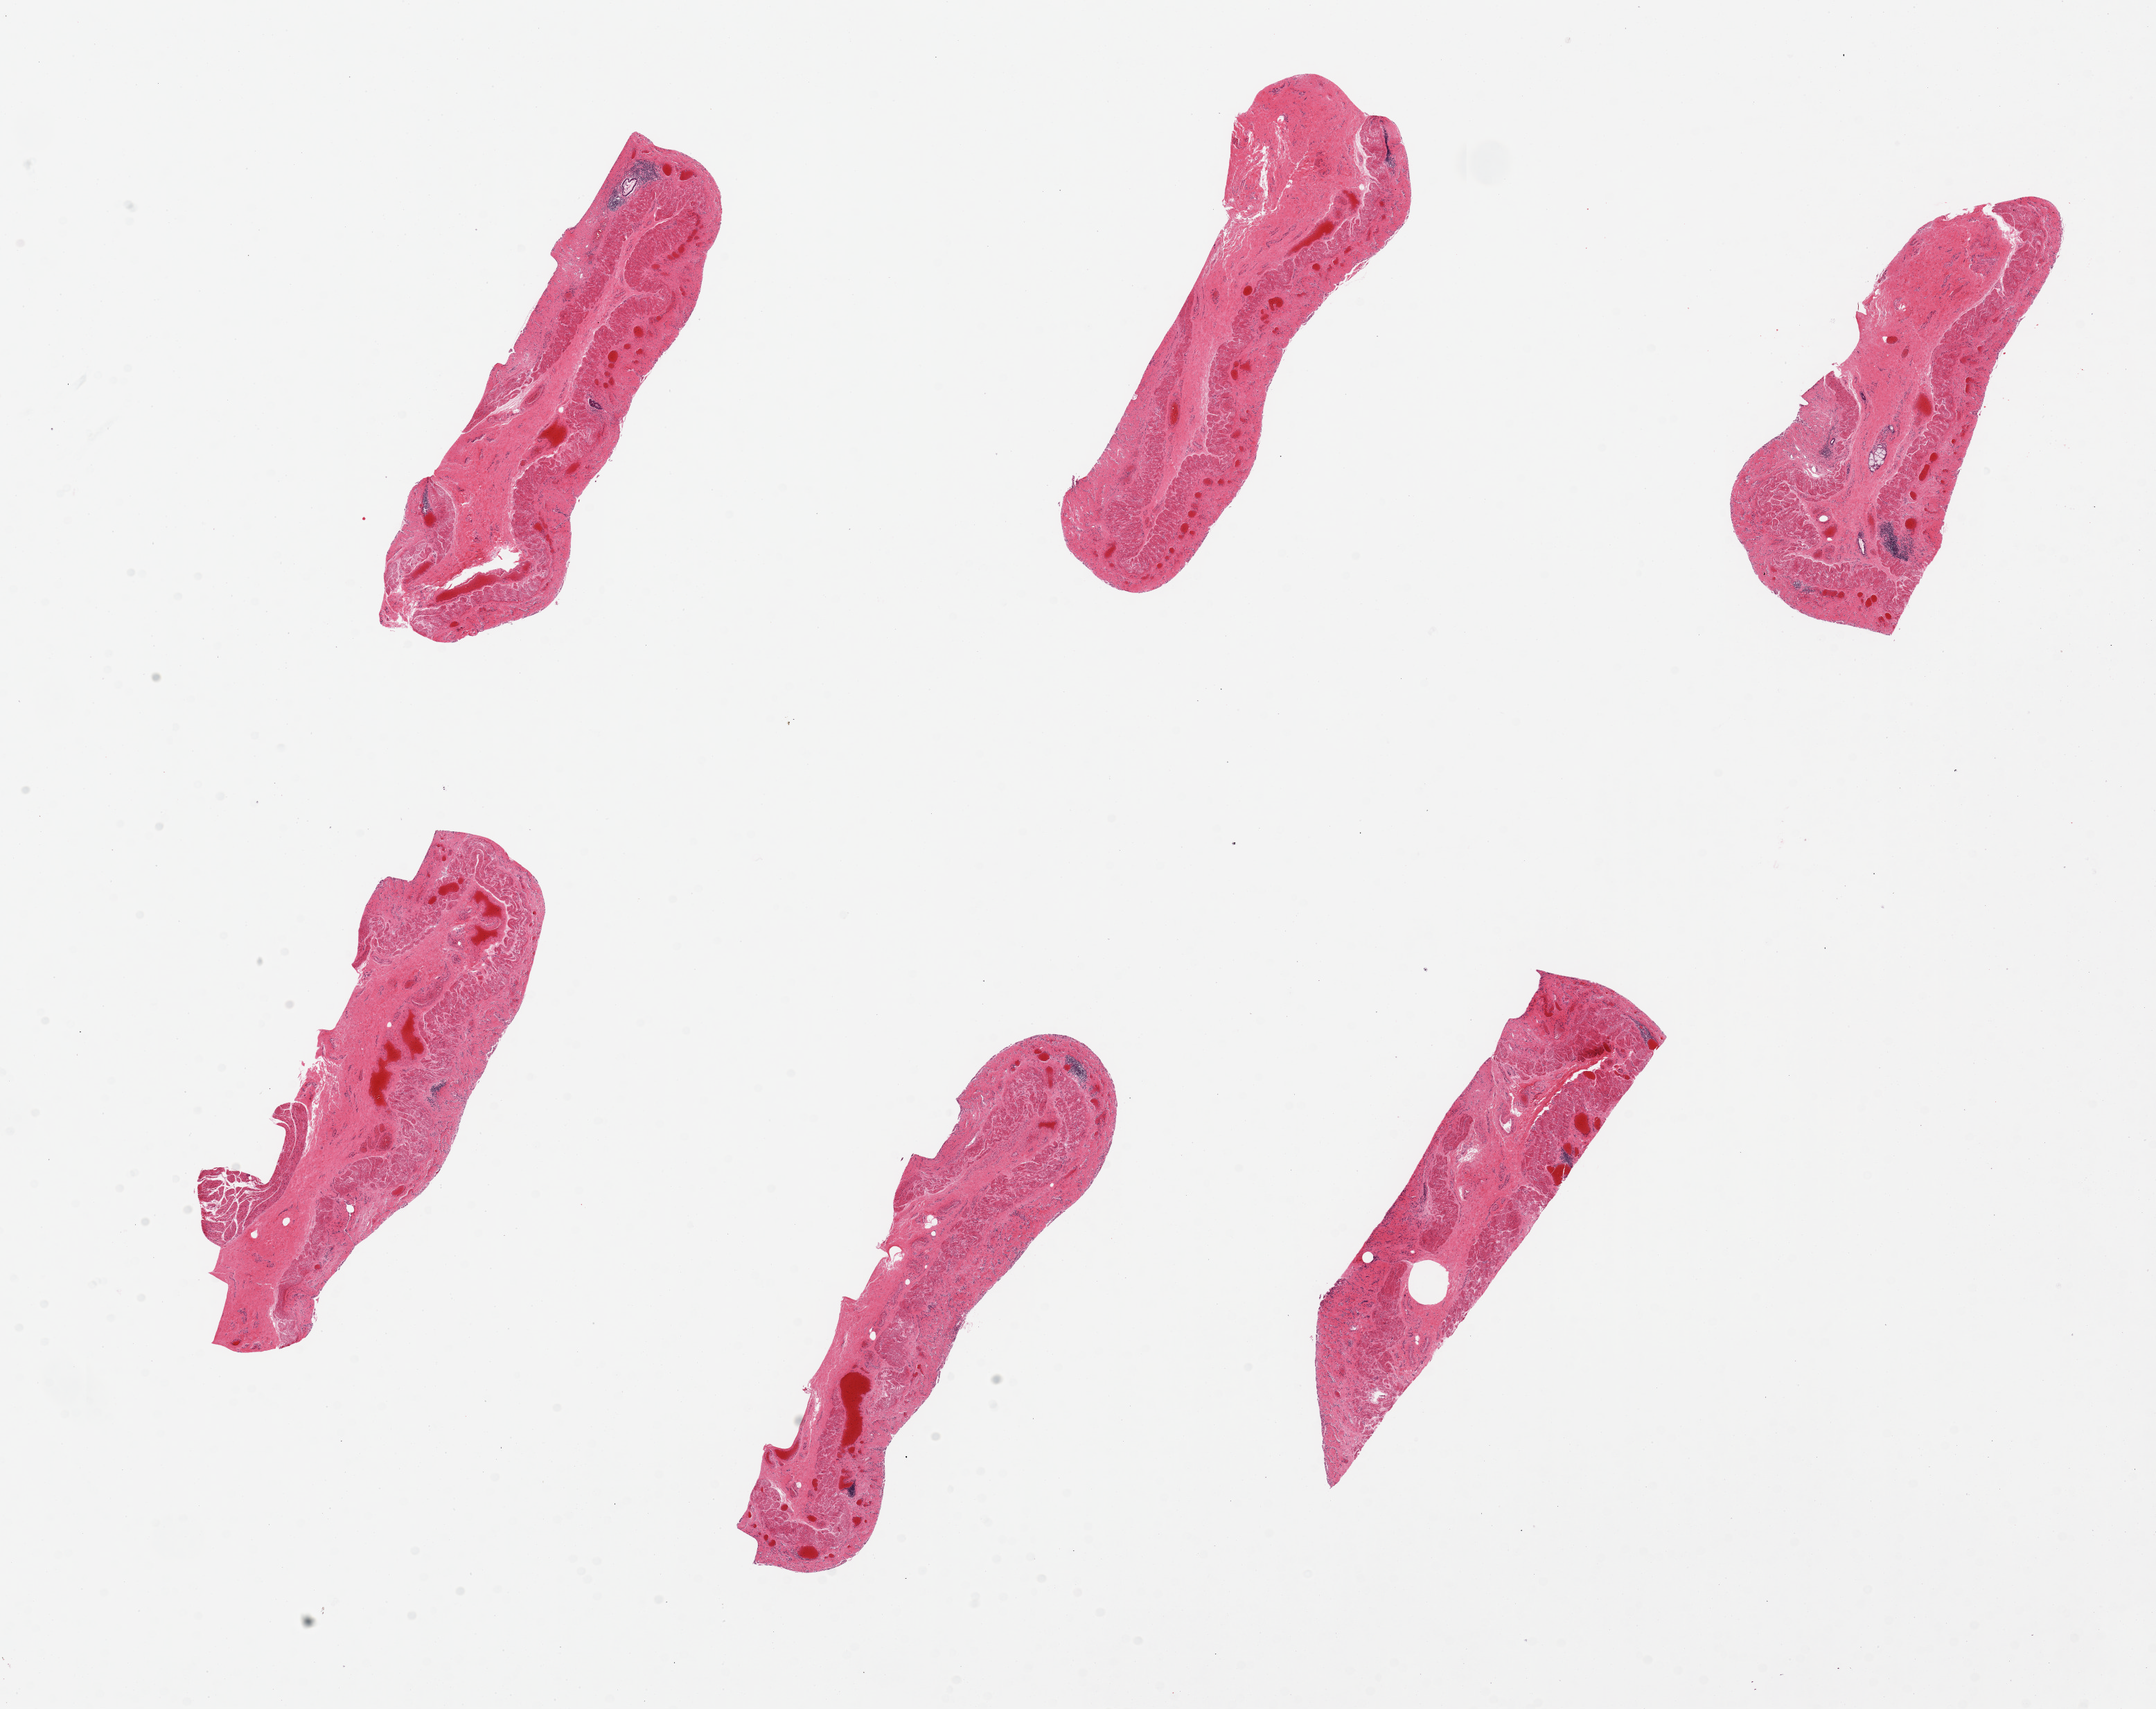
Digitized haematoxylin and eosin-stained section — shown as a low-resolution overview of the whole scanned area (about 24.6 x 19.5 mm); PAXgene-fixed paraffin-embedded (PFPE) section; target tissue: esophageal mucous membrane; donor tissue sample. Donor: male.
Review note (as recorded): 6 pieces. Surface epithelium completely sloughed on all 6 pieces.